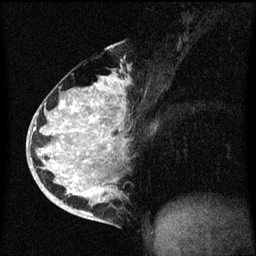
Breast MRI (dynamic contrast-enhanced), one sagittal slice. Dynamic contrast-enhanced series, image 2 of 3 at this slice position (ordered by acquisition). 1.5 T. TE 4.2 ms, TR 8.4 ms. 2 mm slice thickness. 256 × 256 image matrix, field of view 200 × 200 mm. Patient: female, 34 years. From the clinical record (not read from this slice): setting: breast cancer imaged before/during neoadjuvant chemotherapy; receptor status: HR-positive, HER2-negative.
Structures marked on this image (semi-automatically segmented with operator editing):
- analysis volume of interest (the breast-tissue region the enhancement analysis was run in; not a lesion): bounding box [x1, y1, x2, y2] px = [34, 48, 131, 215]
- tumour enhancement mask (voxels above the 70 % enhancement threshold inside the analysis volume of interest): [34, 78, 115, 215]